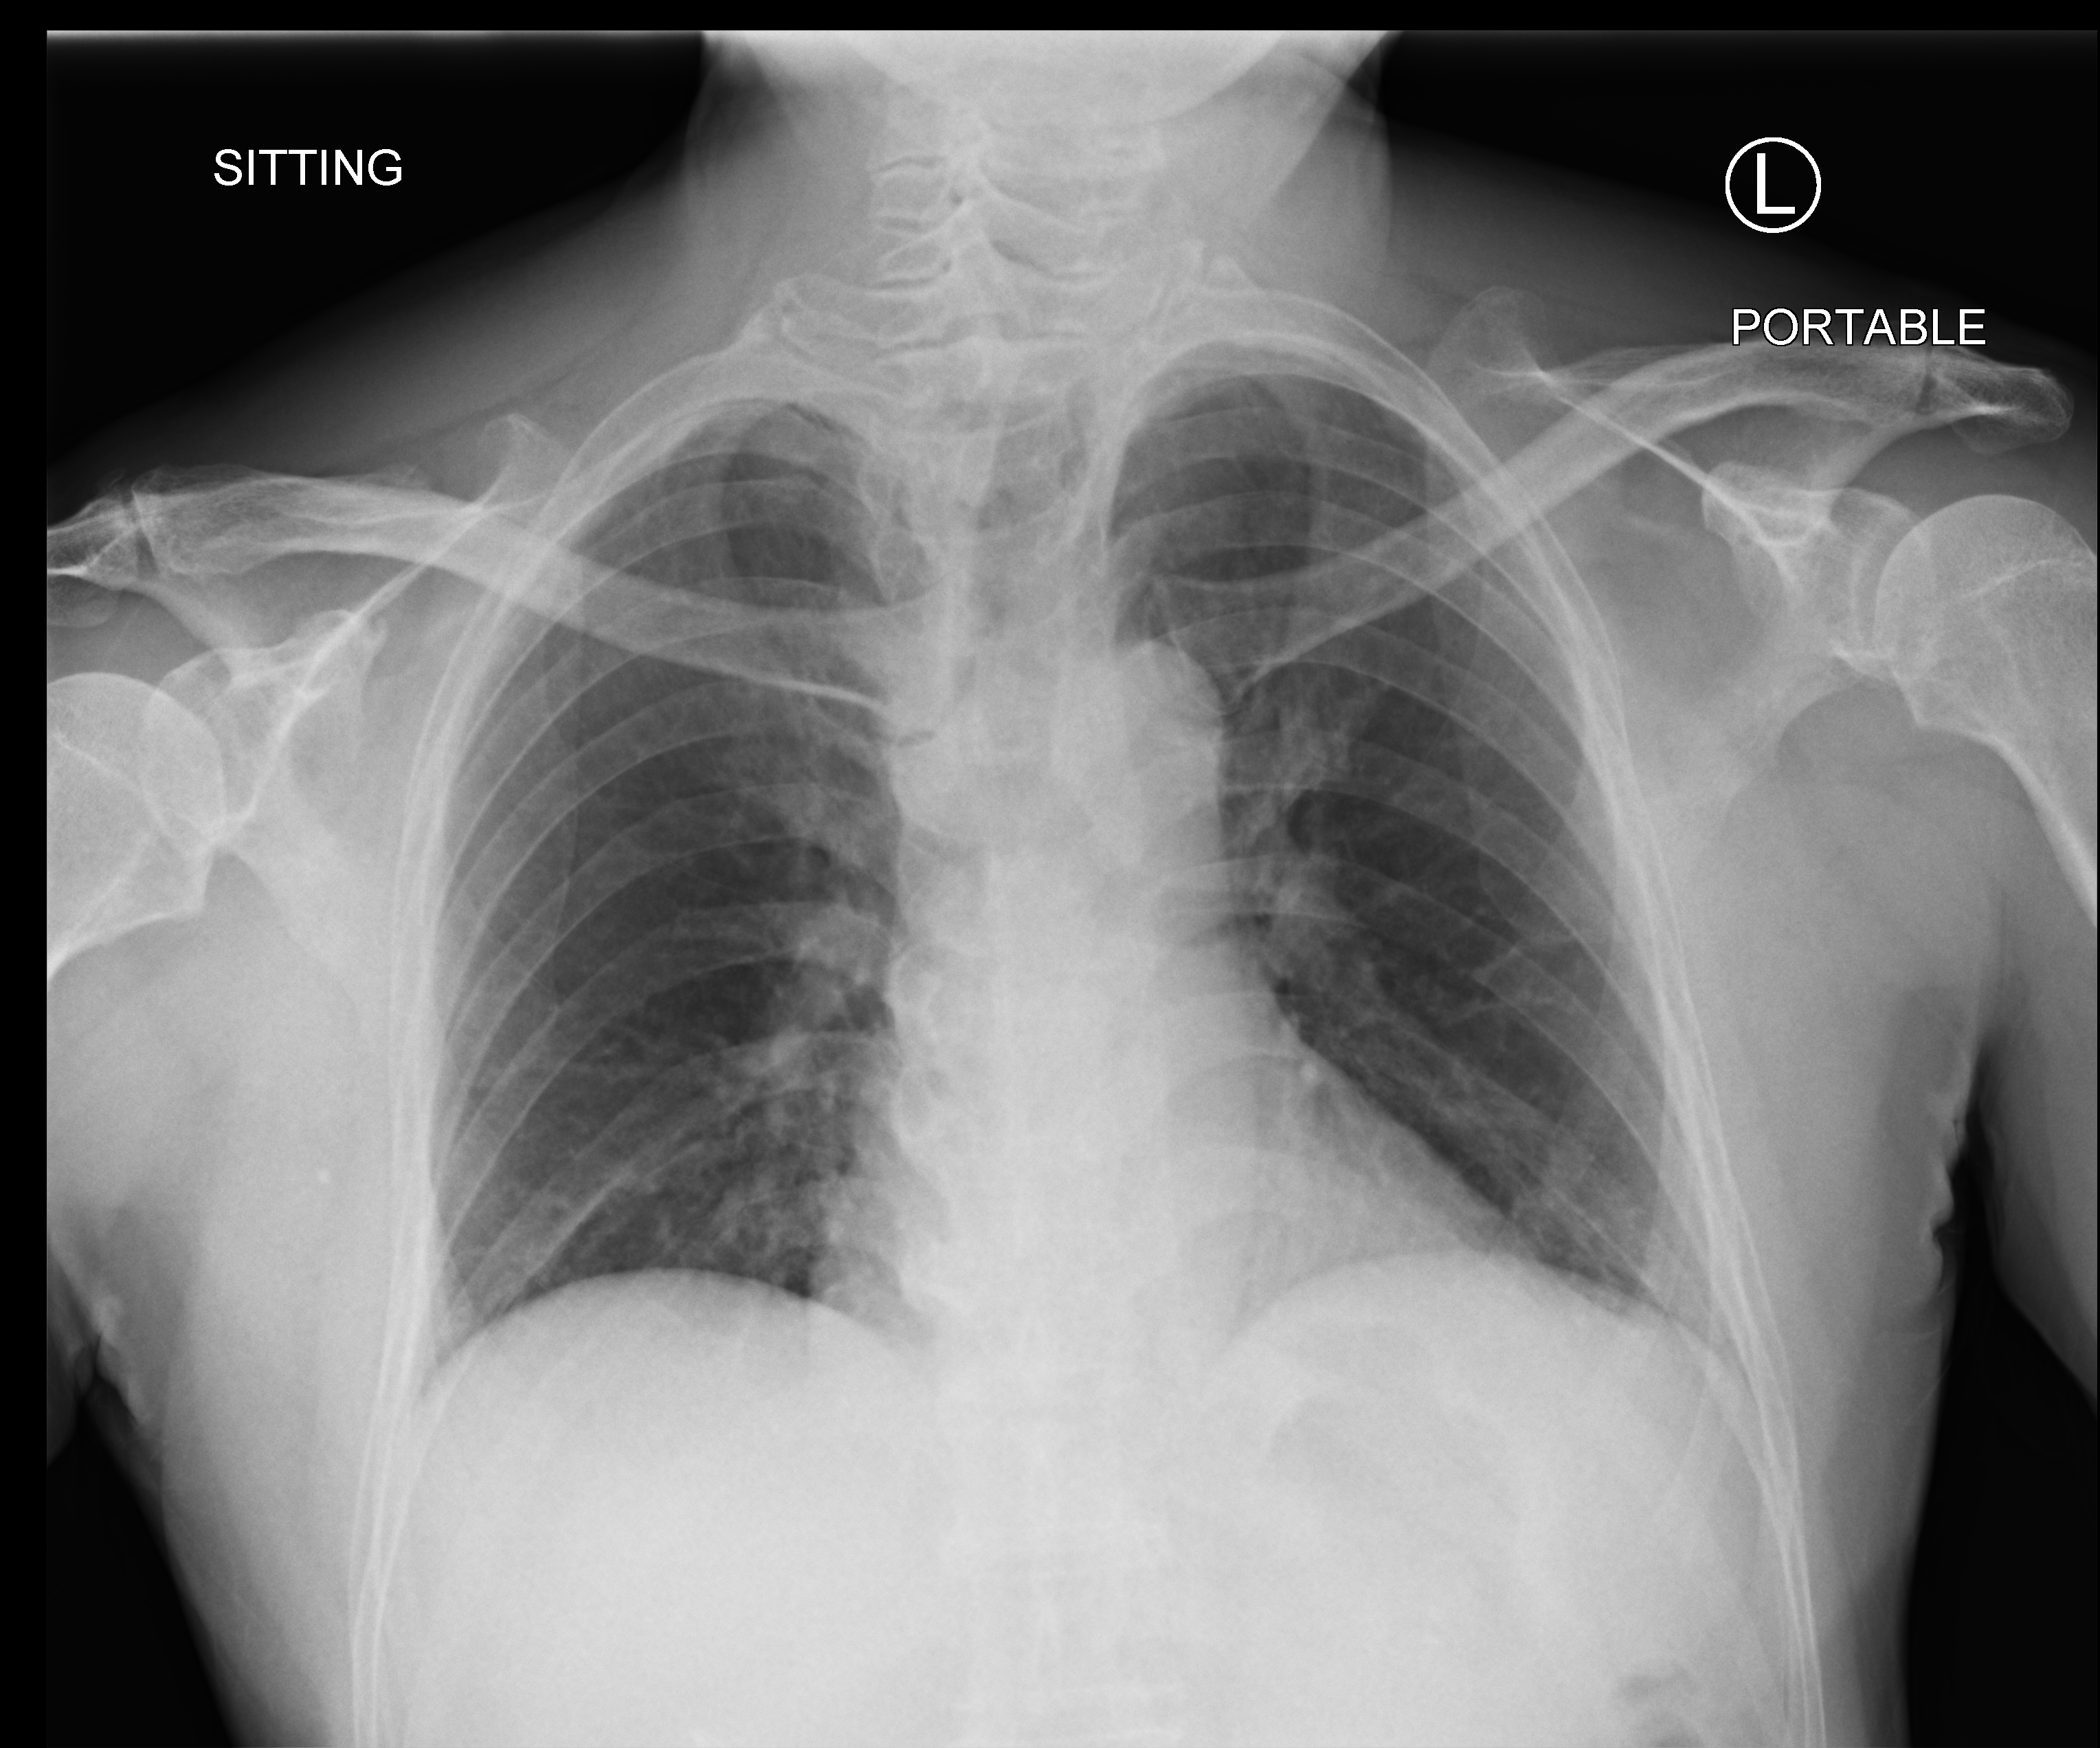
Chest X-ray (portable); anteroposterior (AP) projection. Male patient hospitalised with COVID-19, age 60–74 years.
Hospital-stay facts (about this admission, not read from this image; timing relative to this image not recorded): length of hospital stay: 1 day; mechanically ventilated during this hospital stay: no; admitted to intensive care during this hospital stay: no.